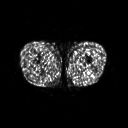
FDG PET of an extremity soft-tissue mass (from a PET/CT study), one axial slice. Position 222 of 267 along the scan axis. 128 × 128 image matrix, field of view 500 × 500 mm. Patient: male, 27 years. Case-level facts recorded for this patient, not image findings: histological type: extraskeletal osteosarcoma; grade: high; site of the primary tumour: left adductur.
Structures marked on this image (expert contour drawn on MRI and transferred to this co-registered scan by the dataset authors):
- gross tumour volume (mass): bounding box <70,62,90,71> (left, top, right, bottom; pixels)